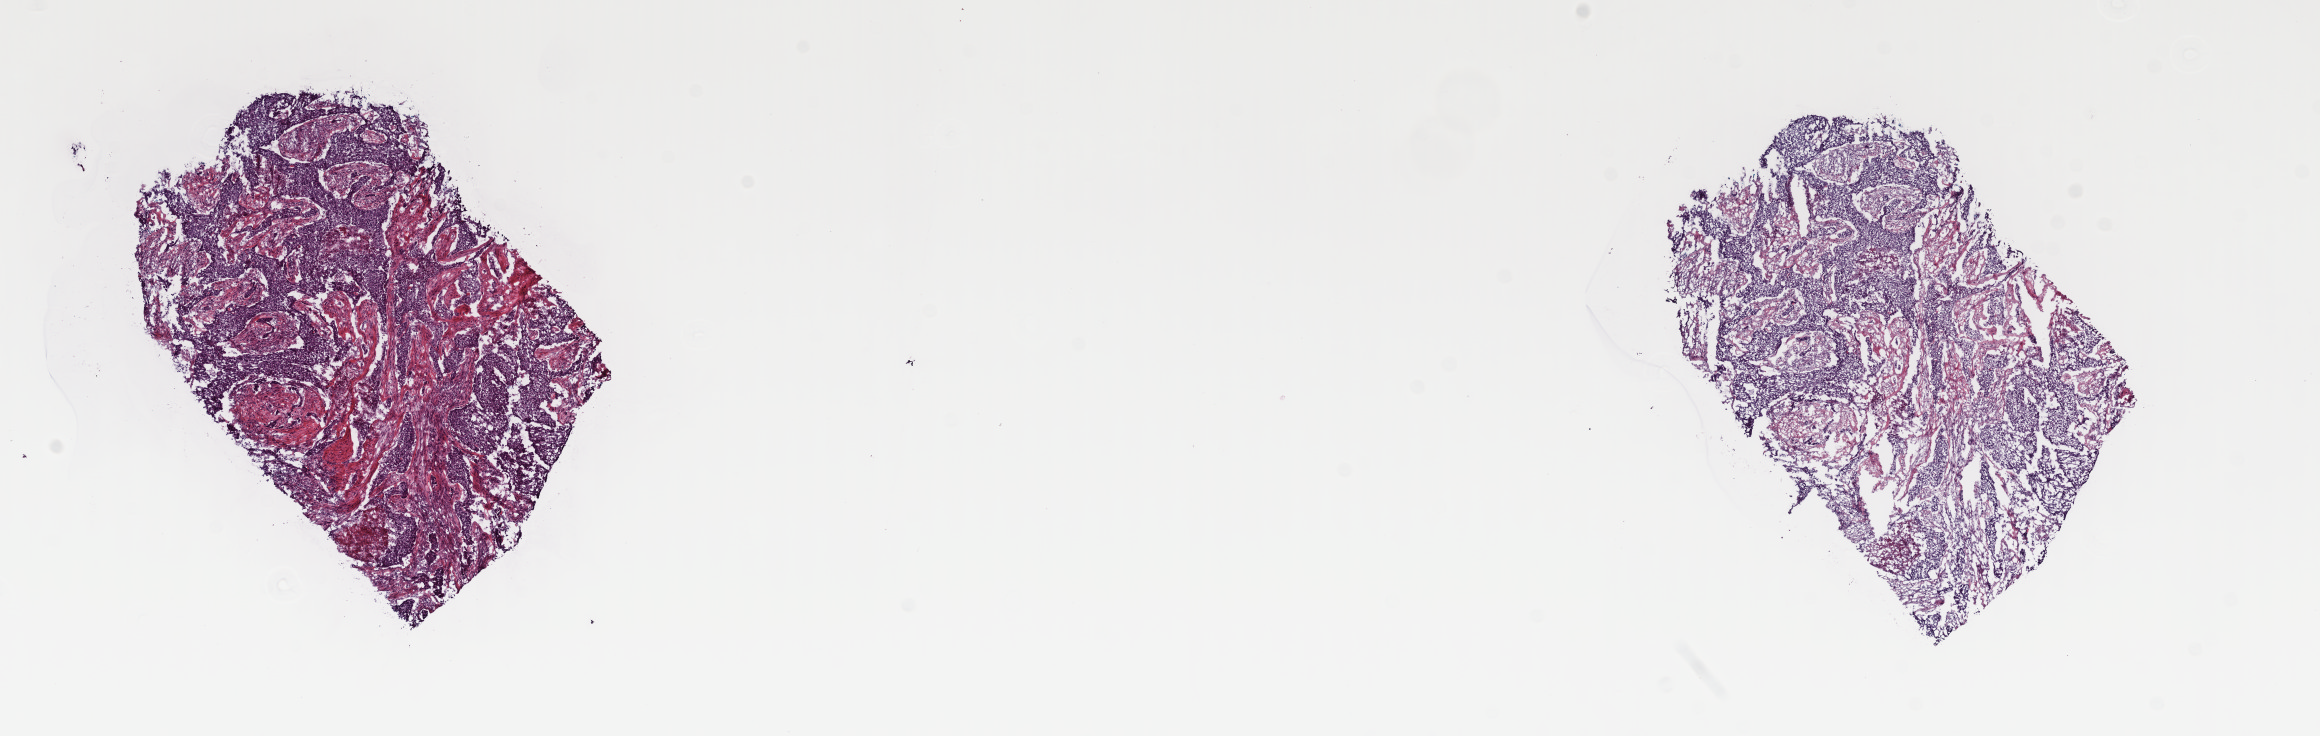
Whole-slide histology image, Hematoxylin and eosin (H&E) stained, low-resolution overview of the scanned area, about 18.3 x 5.8 mm (acquisition: 40x scan), frozen section from the top of the tissue portion, bladder, primary tumour sample. Male patient; age at initial diagnosis 59 years. Histologic grade: high grade. Slide review estimates, as recorded: tumour cells 80%, tumour nuclei 80%, normal cells 0%, stromal cells 20%, necrosis 0%. Infiltration values recorded for this section: lymphocyte infiltration 3%, monocyte infiltration 1%, neutrophil infiltration 2%.
AJCC pathologic stage: II. Diagnosis: Transitional cell carcinoma (dome of bladder). Lymph nodes positive (case pathology): 0 of 8 examined.